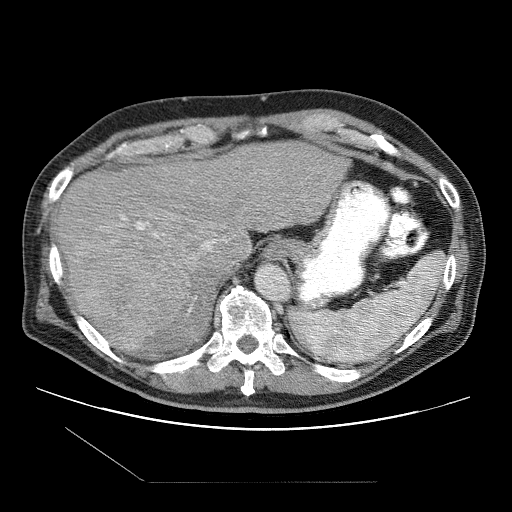
Contrast-enhanced abdominal CT (liver protocol), one axial slice. Position 78 of 109 along the scan axis. Reconstruction kernel STANDARD. 120 kVp. One of 2 acquisitions stored at this slice position. Soft-tissue window (W 400 / L 40 HU). 2.5 mm slice thickness. 512 × 512 image matrix, field of view 400 × 400 mm. From the clinical record (not read from this slice): diagnosis: hepatocellular carcinoma (patient treated with transarterial chemoembolisation; whether this scan precedes or follows treatment is not stated here); TNM stage (as recorded): Stage-IIIB.
Structures marked on this image (semi-automatic segmentation, software-assisted and operator-edited):
- liver parenchyma outside the tumour (the mass and vessels are separate outlines, so this box may not span the whole liver): bounding box <54,142,348,350> (left, top, right, bottom; pixels)
- mass: <69,225,190,355>
- liver vessels: <120,215,223,312>